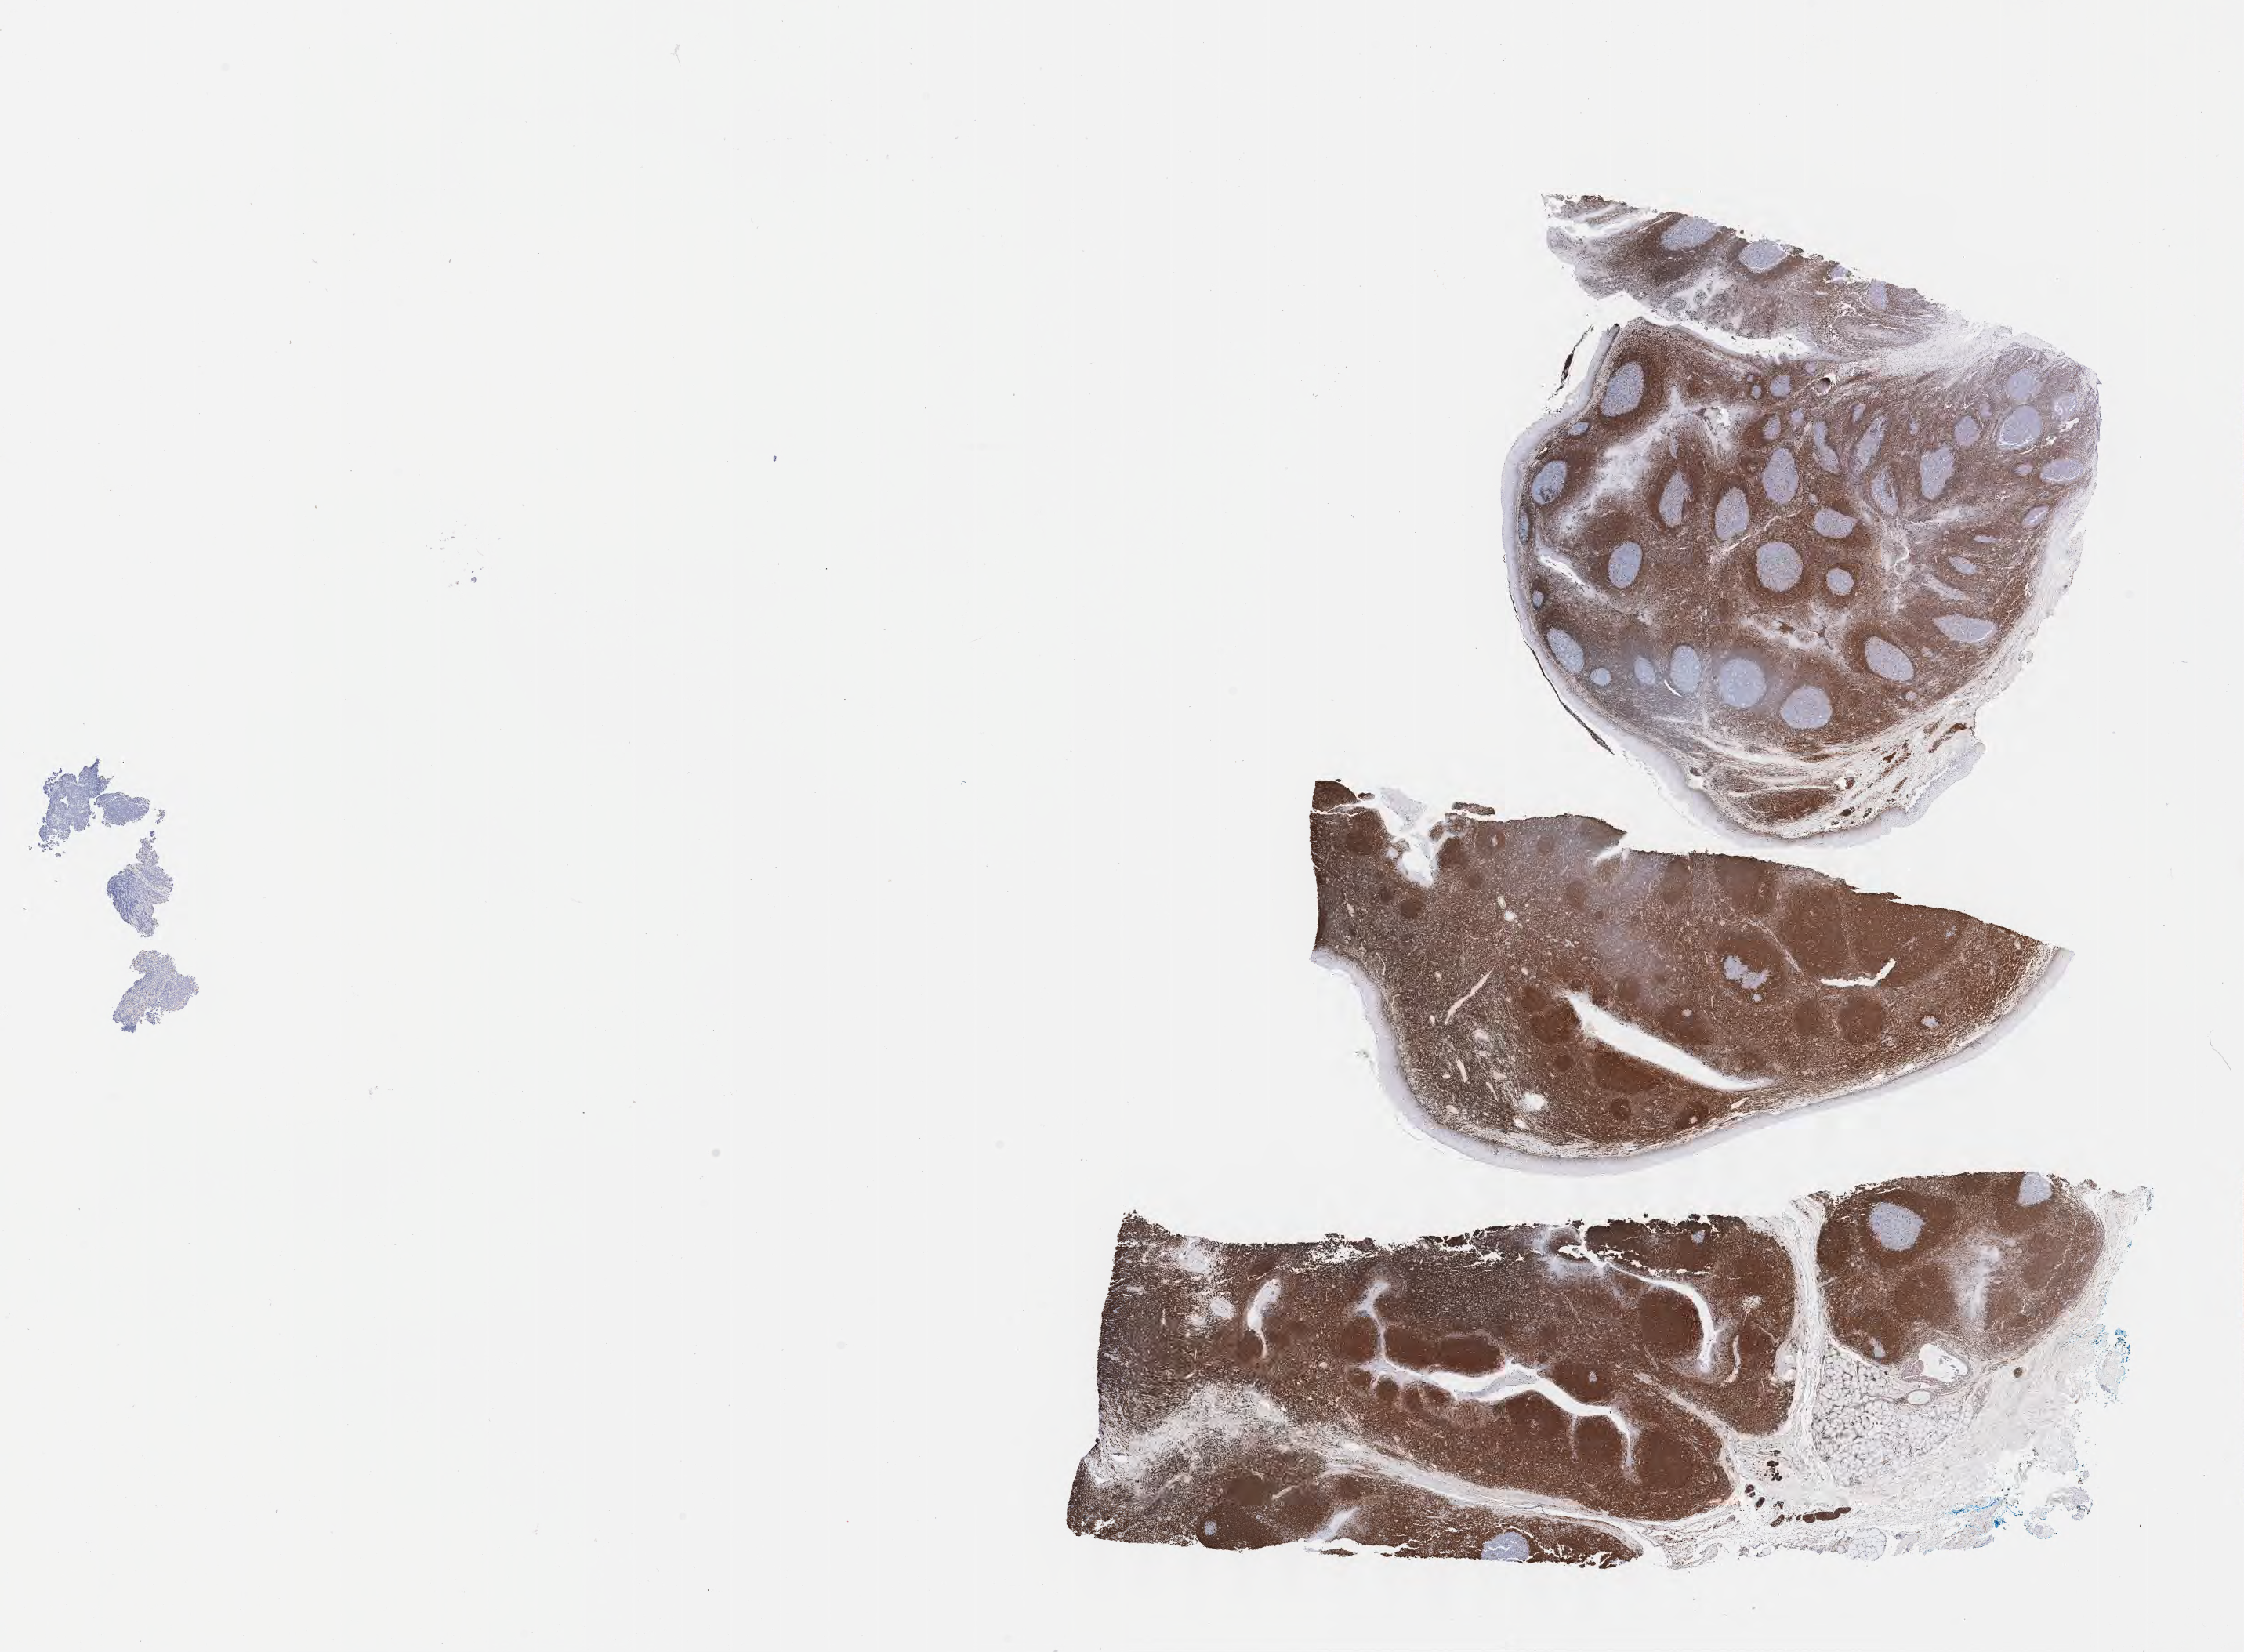
Whole-slide image, immunohistochemical stain for BCL2, shown as a low-resolution overview of the whole scanned area (about 23.1 x 17.0 mm); tumor tissue; site: abdomen proper. Patient: male, age at initial diagnosis 6 years.
Histologic diagnosis: Burkitt lymphoma, NOS.